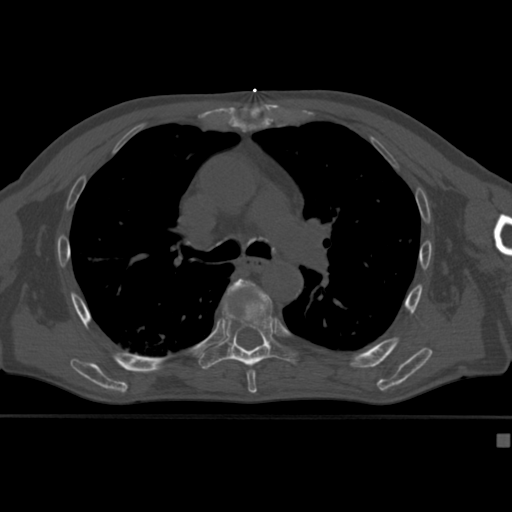
CT including the spine, one axial slice; reconstruction kernel Br40s; bone window (W 1800 / L 400 HU); 1.5 mm slice thickness; 512 × 512 image matrix. Male patient, age 64 years. From the clinical record (not read from this slice): primary cancer: uterus; vertebrae with lytic lesions (as recorded): T1, T4, T5, T7, L5.
Annotated regions visible in this slice (semi-automatic segmentation, software-assisted and operator-edited):
- T6 vertebra: bounding box [x1, y1, x2, y2] px = [223, 278, 258, 382]
- T7 vertebra: [198, 293, 296, 370]